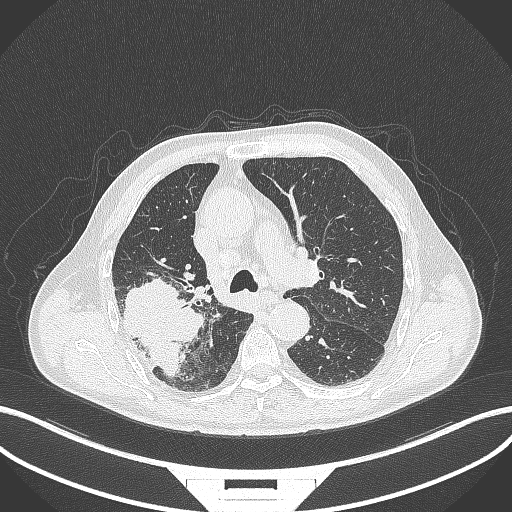
Chest CT, one axial slice. Position 271 of 429 along the scan axis. 120 kVp. Lung window (W 1500 / L -600 HU). 1 mm slice thickness. 512 × 512 image matrix, field of view 400 × 400 mm. Patient: male, 72 years. Case-level facts recorded for this patient, not image findings: clinical TNM (as recorded): T3 N2 M0.
Structures marked on this image (rectangle marked by the reading radiologist):
- lung tumour (recorded histology: adenocarcinoma): bounding box (x1, y1, x2, y2) in pixels: (113, 275, 203, 382)